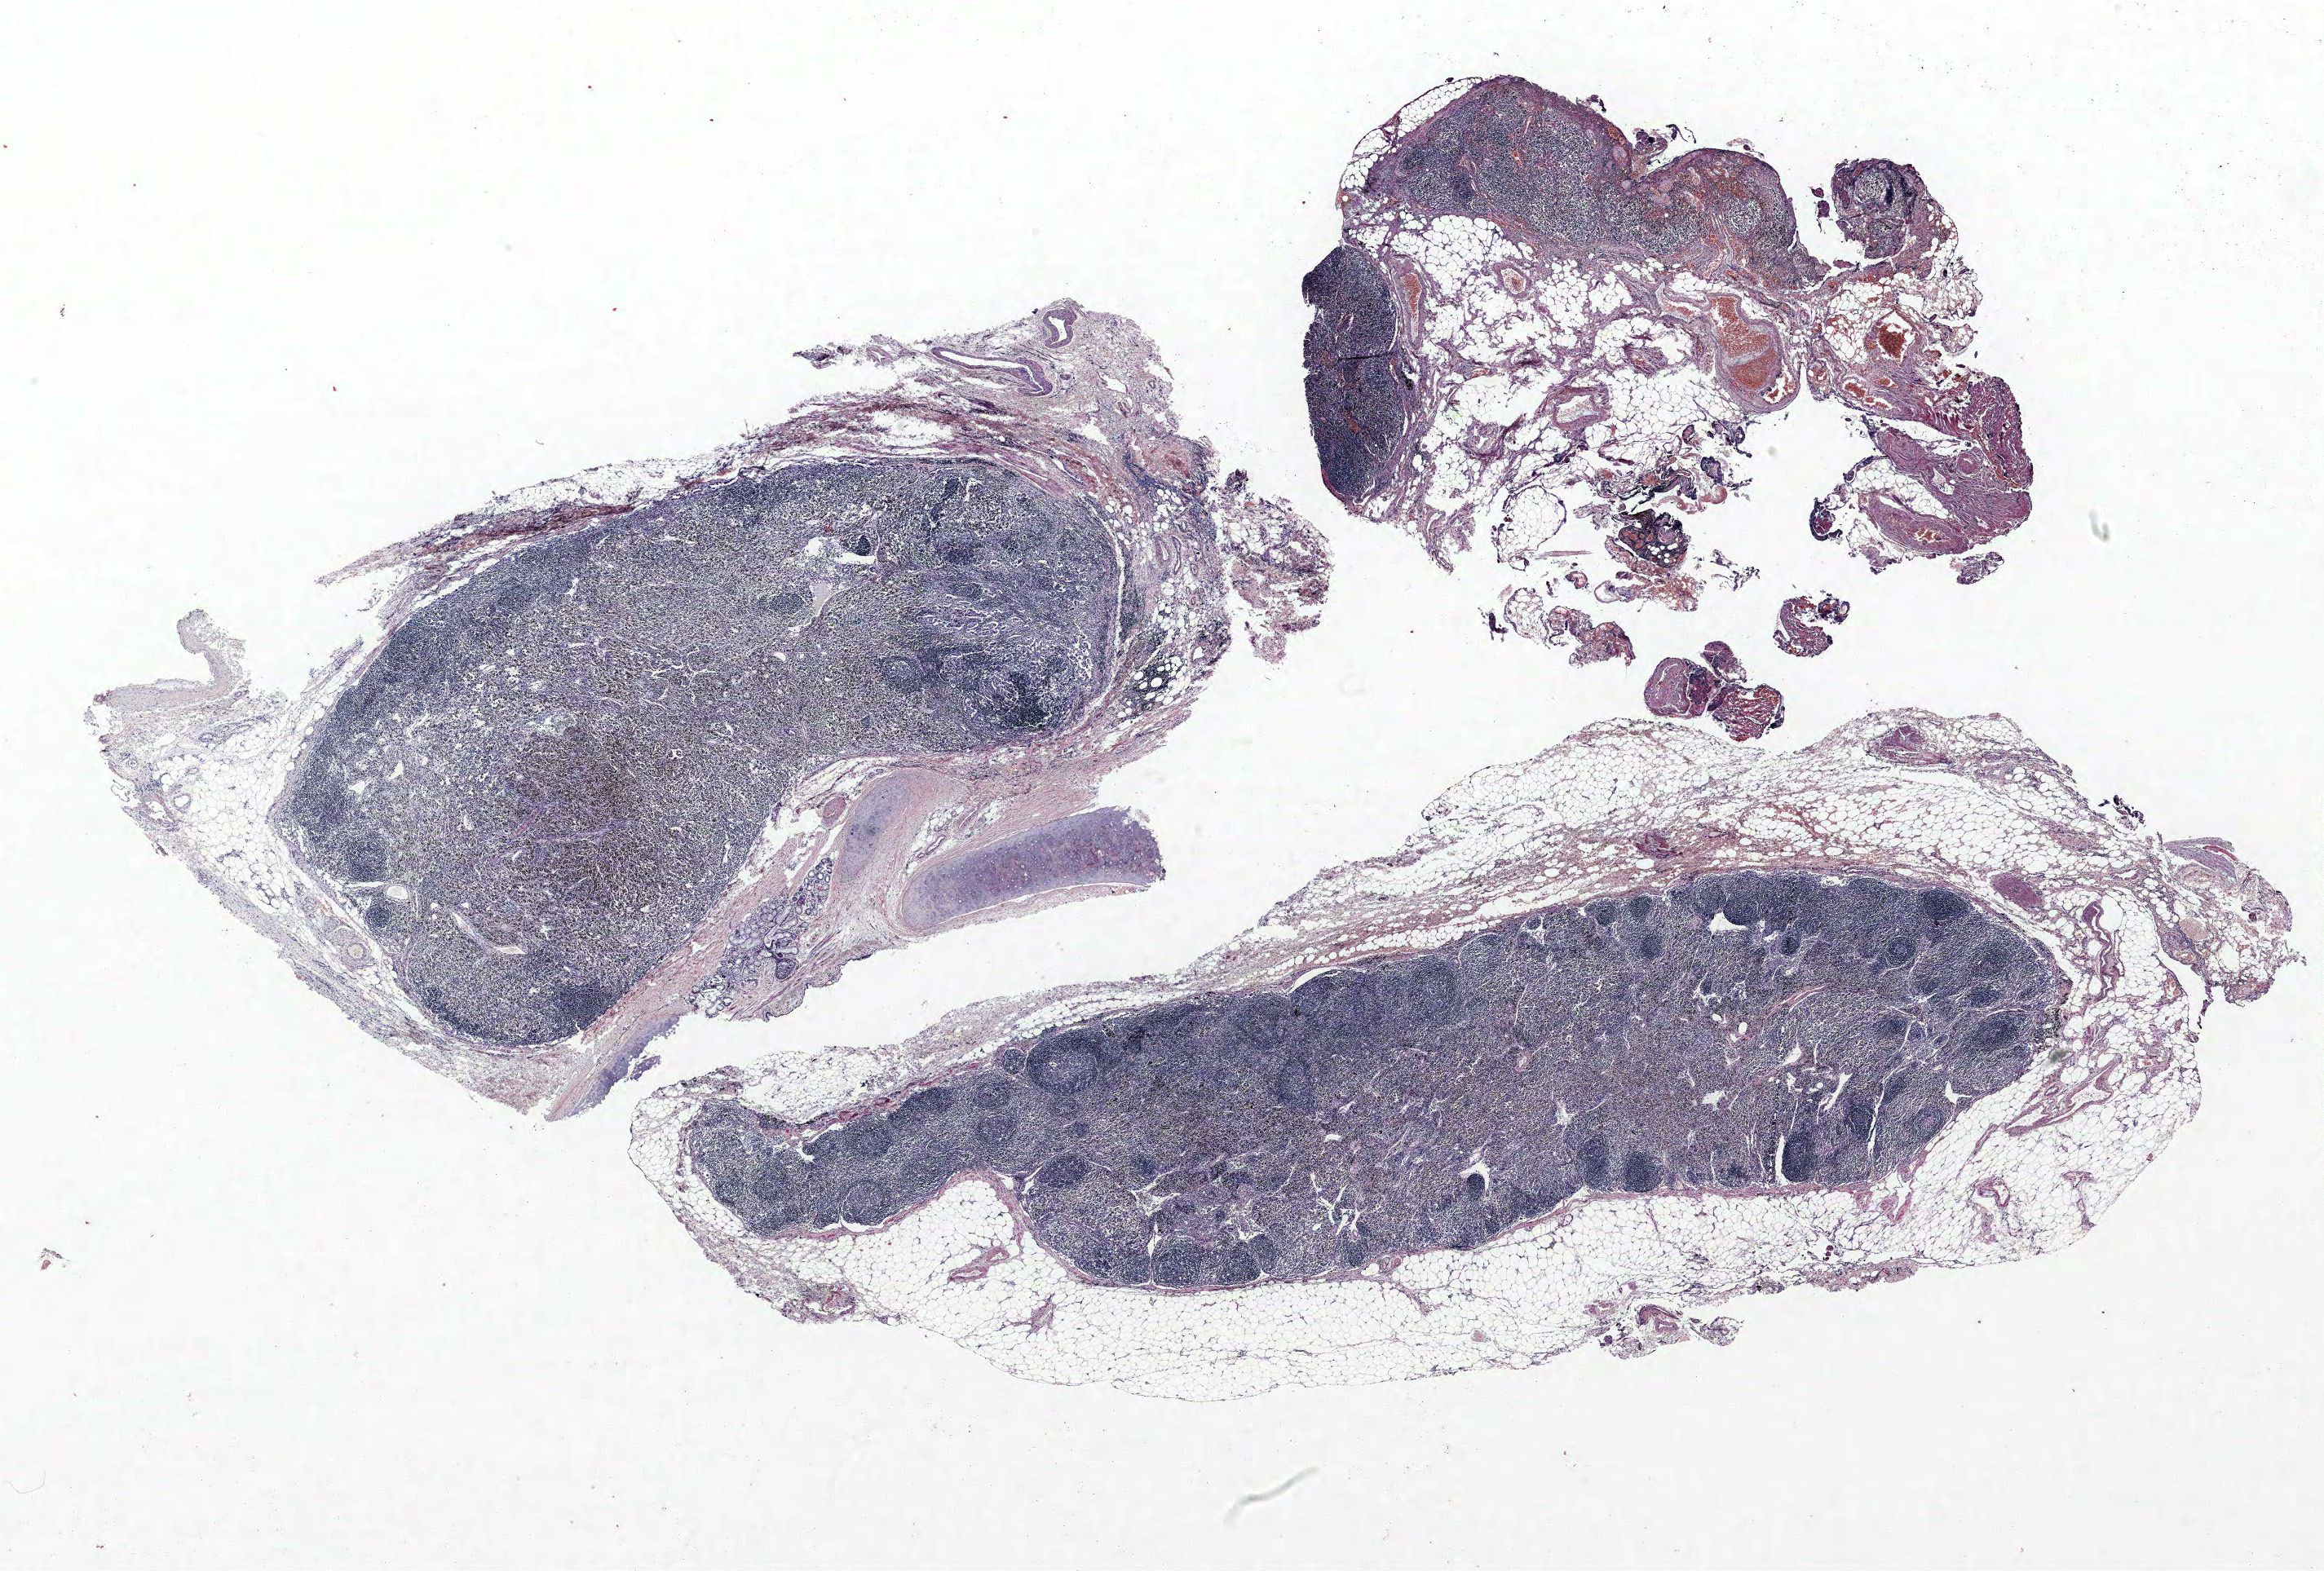
H&E whole-slide image, whole scanned area (about 22.8 x 15.4 mm) shown as a low-resolution overview. FFPE section. Lung tissue. Male patient, aged 71 at enrolment. Grade: moderately differentiated (G2).
• tumour size (pathology): 25 mm
• stage (AJCC 6th edition): IIIA
• participant's lung-cancer diagnosis: Bronchiolo-alveolar adenocarcinoma, NOS
• primary tumour location (clinical record): right upper lobe